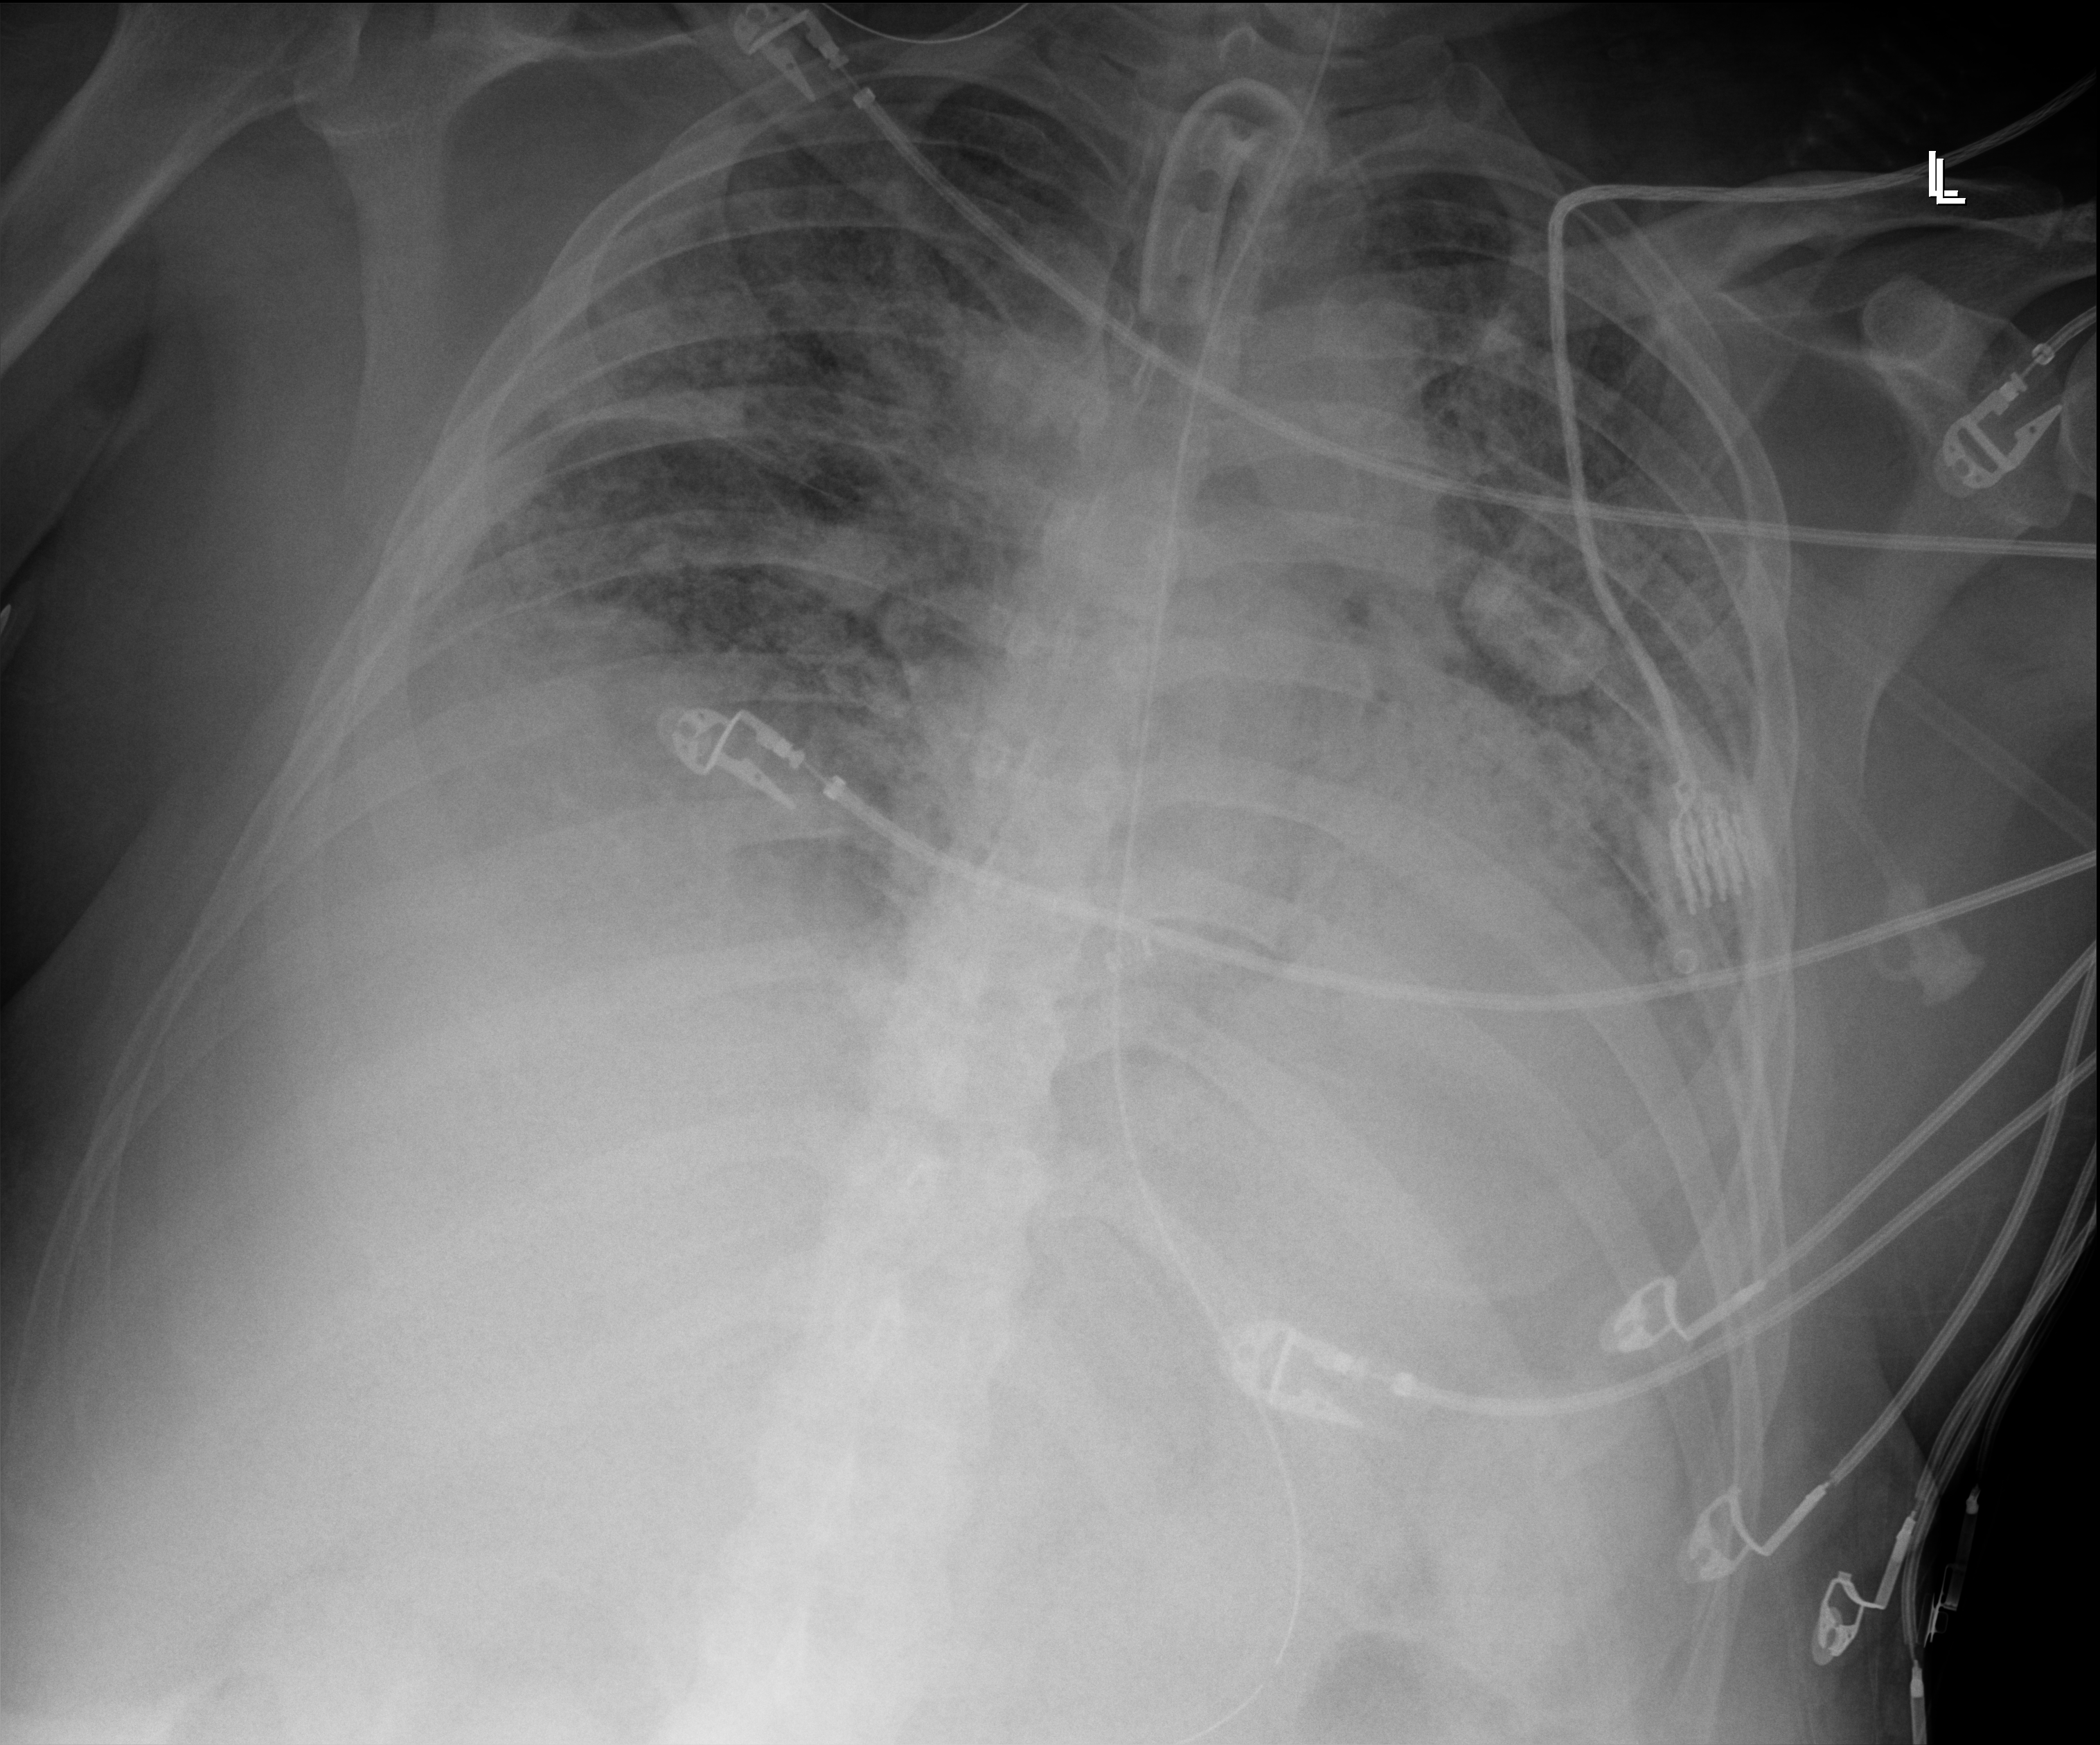
Chest X-ray (portable). Male patient hospitalised with COVID-19, age 18–59 years.
Hospital-stay facts (about this admission, not read from this image; timing relative to this image not recorded):
- admitted to intensive care during this hospital stay: yes
- length of hospital stay: 96 days